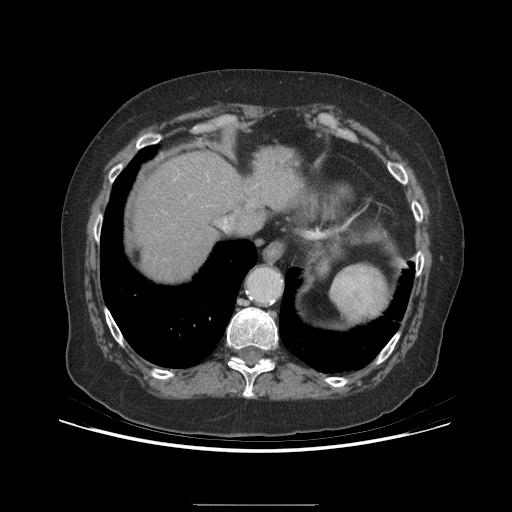
Contrast-enhanced abdominal CT (liver protocol), one axial slice. Reconstruction kernel STANDARD. Soft-tissue window (W 400 / L 40 HU). 512 × 512 image matrix, field of view 400 × 400 mm. Case-level facts recorded for this patient, not image findings: diagnosis: hepatocellular carcinoma (patient treated with transarterial chemoembolisation; whether this scan precedes or follows treatment is not stated here); TNM stage (as recorded): Stage-I; Child-Pugh class: A; tumour differentiation: moderately differentiated; tumour nodularity: uninodular.
Annotated regions visible in this slice (semi-automatic segmentation, software-assisted and operator-edited):
- abdominal aorta: bounding box <247,267,281,301> (left, top, right, bottom; pixels)
- liver parenchyma outside the tumour (the mass and vessels are separate outlines, so this box may not span the whole liver): <134,148,304,280>